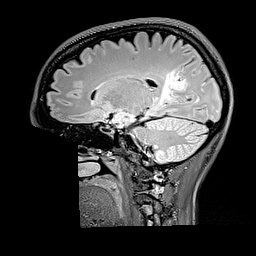
Brain MRI from a brain-tumour surgery series, one sagittal slice. Position 103 of 176 along the scan axis. T2 FLAIR. 1 mm slice thickness. 256 × 256 image matrix. From the clinical record (not read from this slice): histopathology: Oligodendroglioma; WHO grade: 2; IDH mutation: yes; tumour location: Right Parietal.
Annotated regions visible in this slice (manually delineated by an expert):
- tumour: box from (x=159, y=68) to (x=187, y=104) px